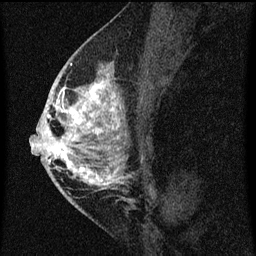
Breast MRI (dynamic contrast-enhanced), one sagittal slice; position 33 of 60 along the scan axis; dynamic contrast-enhanced series, image 2 of 3 at this slice position (ordered by acquisition); 1.5 T; TE 4.2 ms, TR 8 ms; 256 × 256 image matrix. Patient: female, 46 years.
Annotated regions visible in this slice (semi-automatically segmented with operator editing):
- analysis volume of interest (the breast-tissue region the enhancement analysis was run in; not a lesion): bounding box (x1, y1, x2, y2) in pixels: (48, 68, 124, 195)
- tumour enhancement mask (voxels above the 70 % enhancement threshold inside the analysis volume of interest): (48, 68, 123, 189)